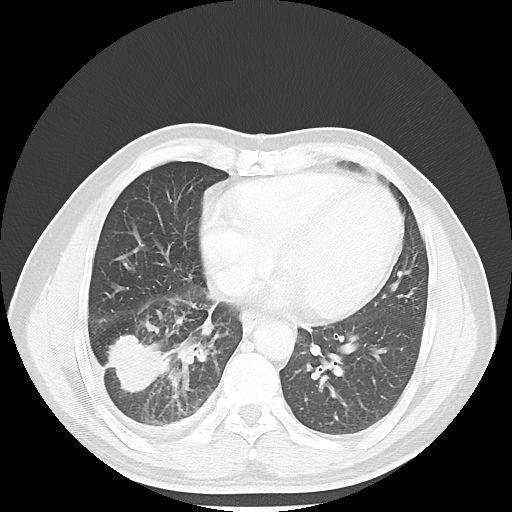
Chest CT, one axial slice; slice 21 of 56 in the series (ordered by position); reconstruction kernel LUNG; 120 kVp; lung window (W 1500 / L -600 HU); 5 mm slice thickness; 512 × 512 image matrix, field of view 344 × 344 mm. Patient: male, 56 years. From the clinical record (not read from this slice): clinical TNM (as recorded): T2 N3 M1.
Structures marked on this image (bounding box drawn by a radiologist):
- lung tumour (recorded histology: adenocarcinoma): bounding box <101,332,172,398> (left, top, right, bottom; pixels)